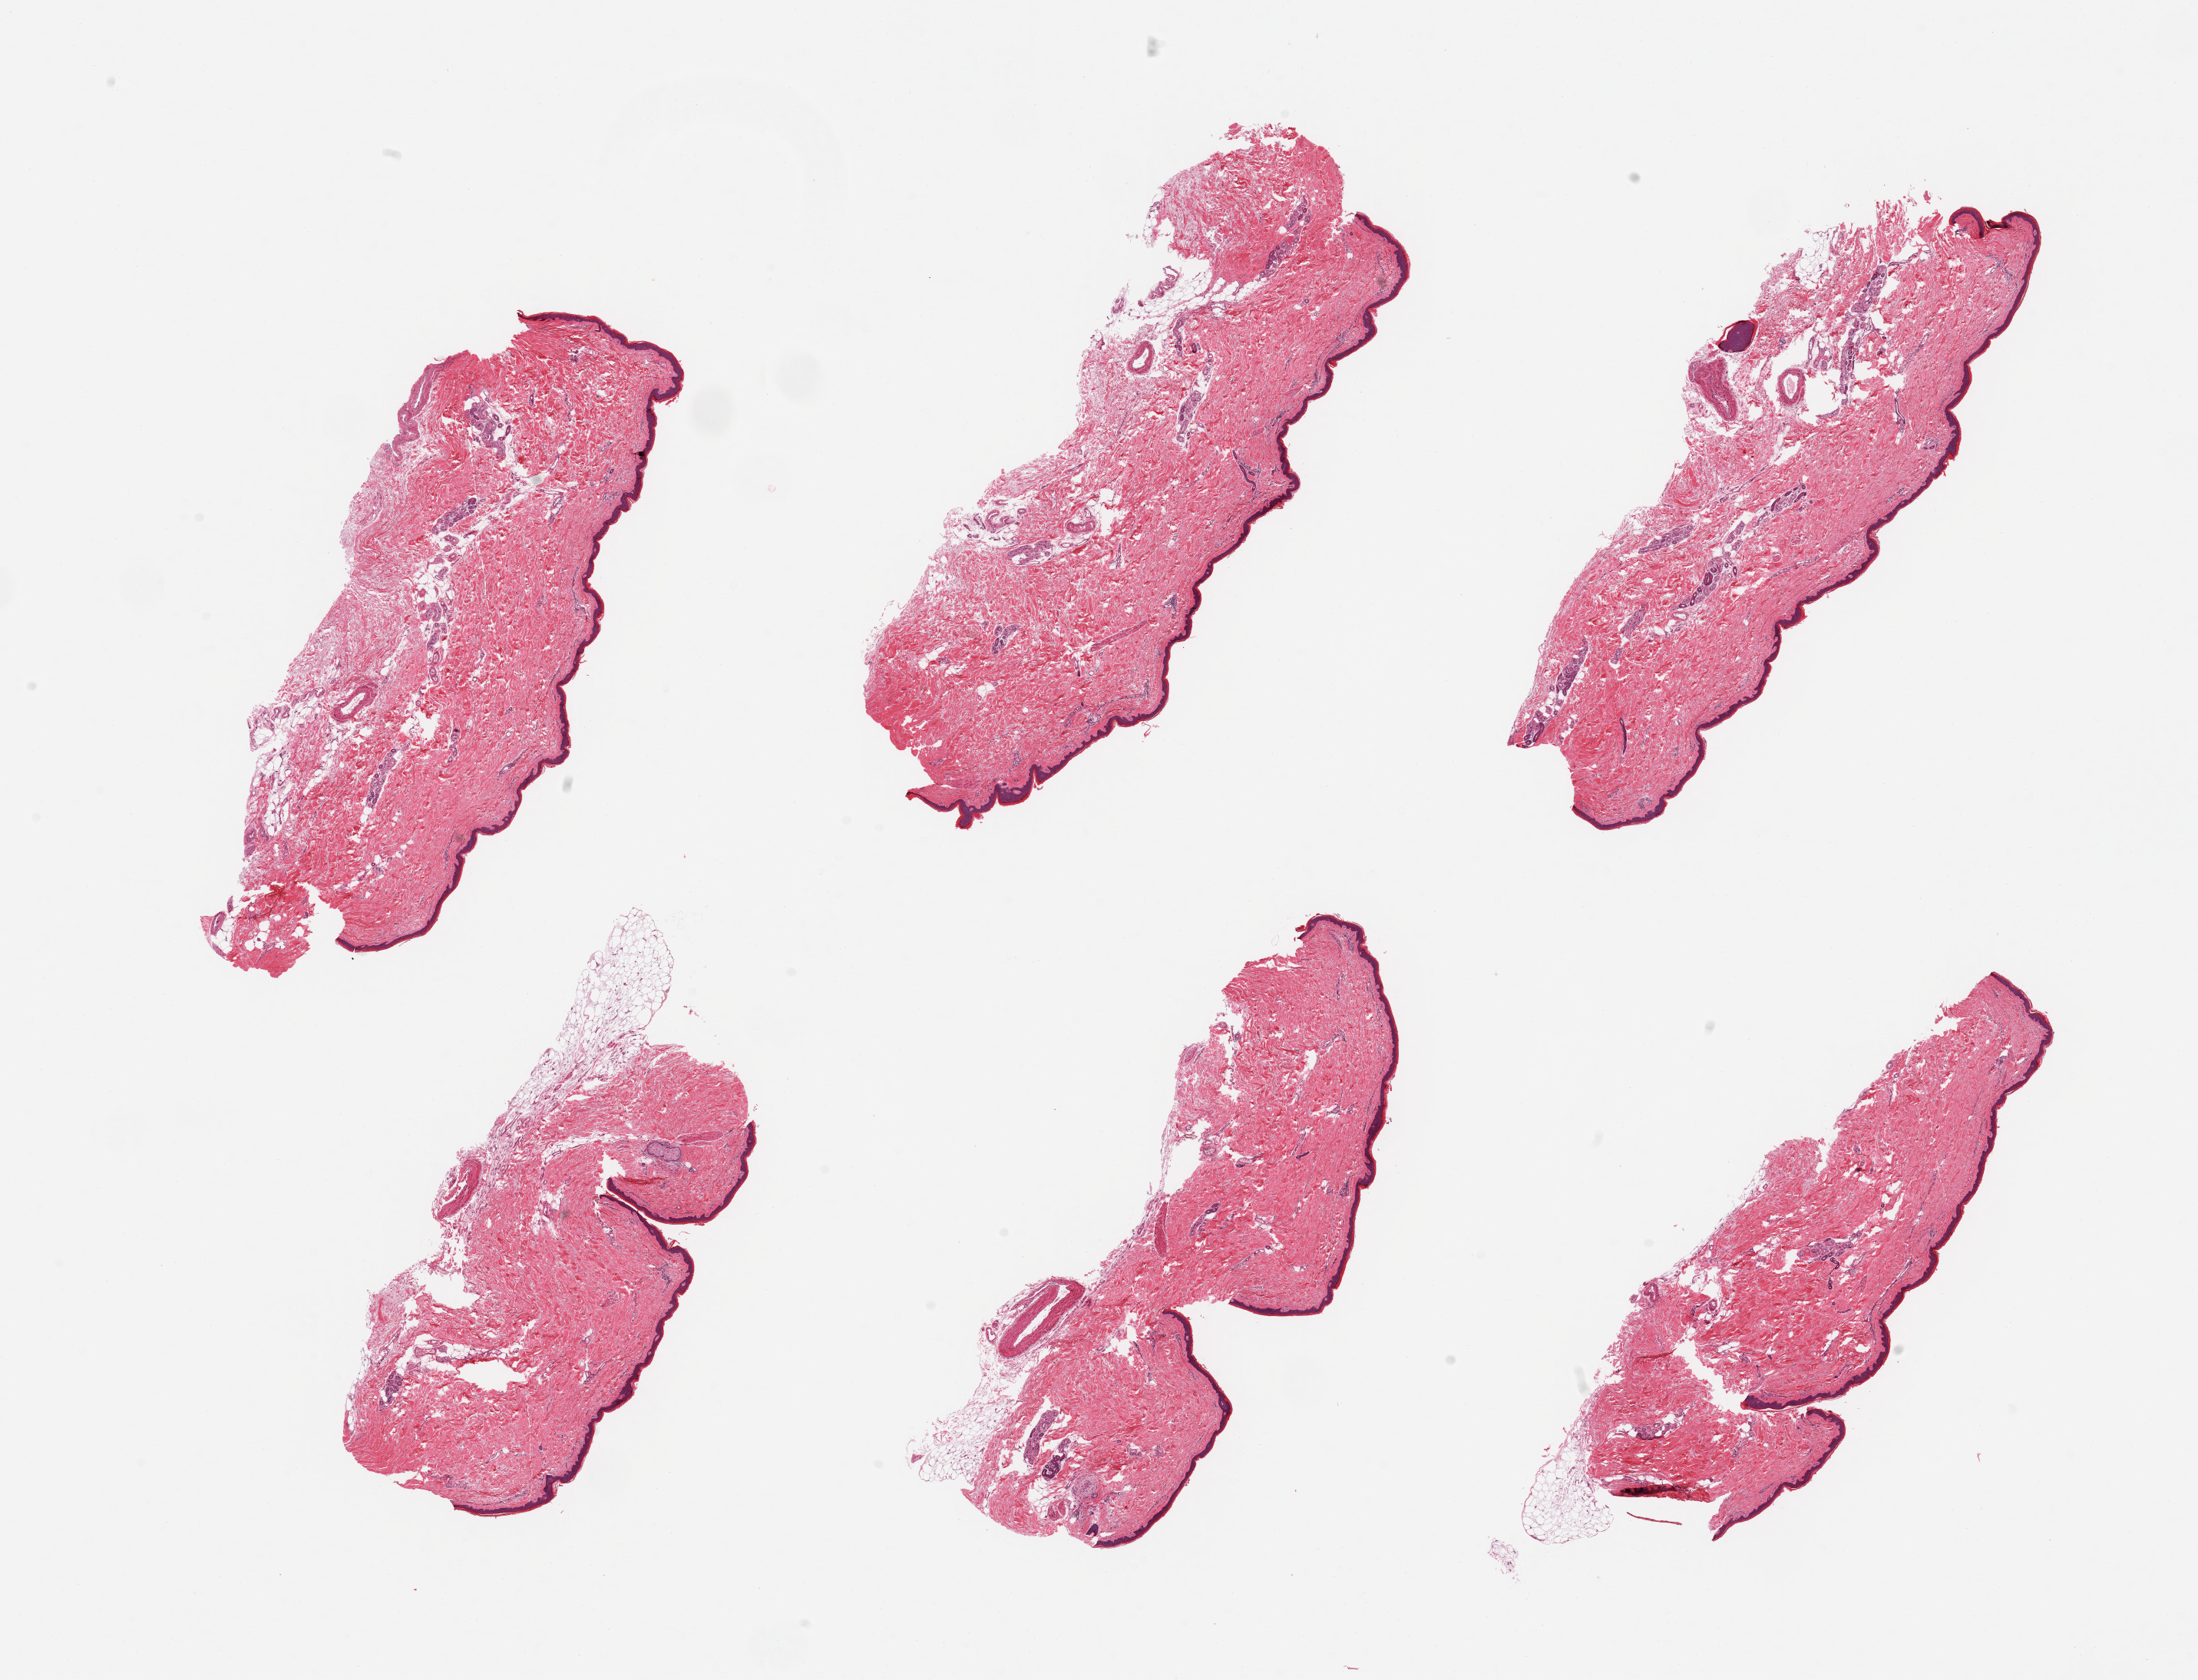
Whole-slide image, haematoxylin and eosin stain, shown as a low-resolution overview of the whole scanned area (about 22.6 x 17.3 mm, from a 20x scan); PAXgene-fixed paraffin-embedded (PFPE) section; sampled site (target tissue): skin of lower leg; donor tissue sample. Male donor.
Pathologist's review note for this sample: 6 pieces; up to 10% predominantly attached fat, epidermis measures 34 microns.